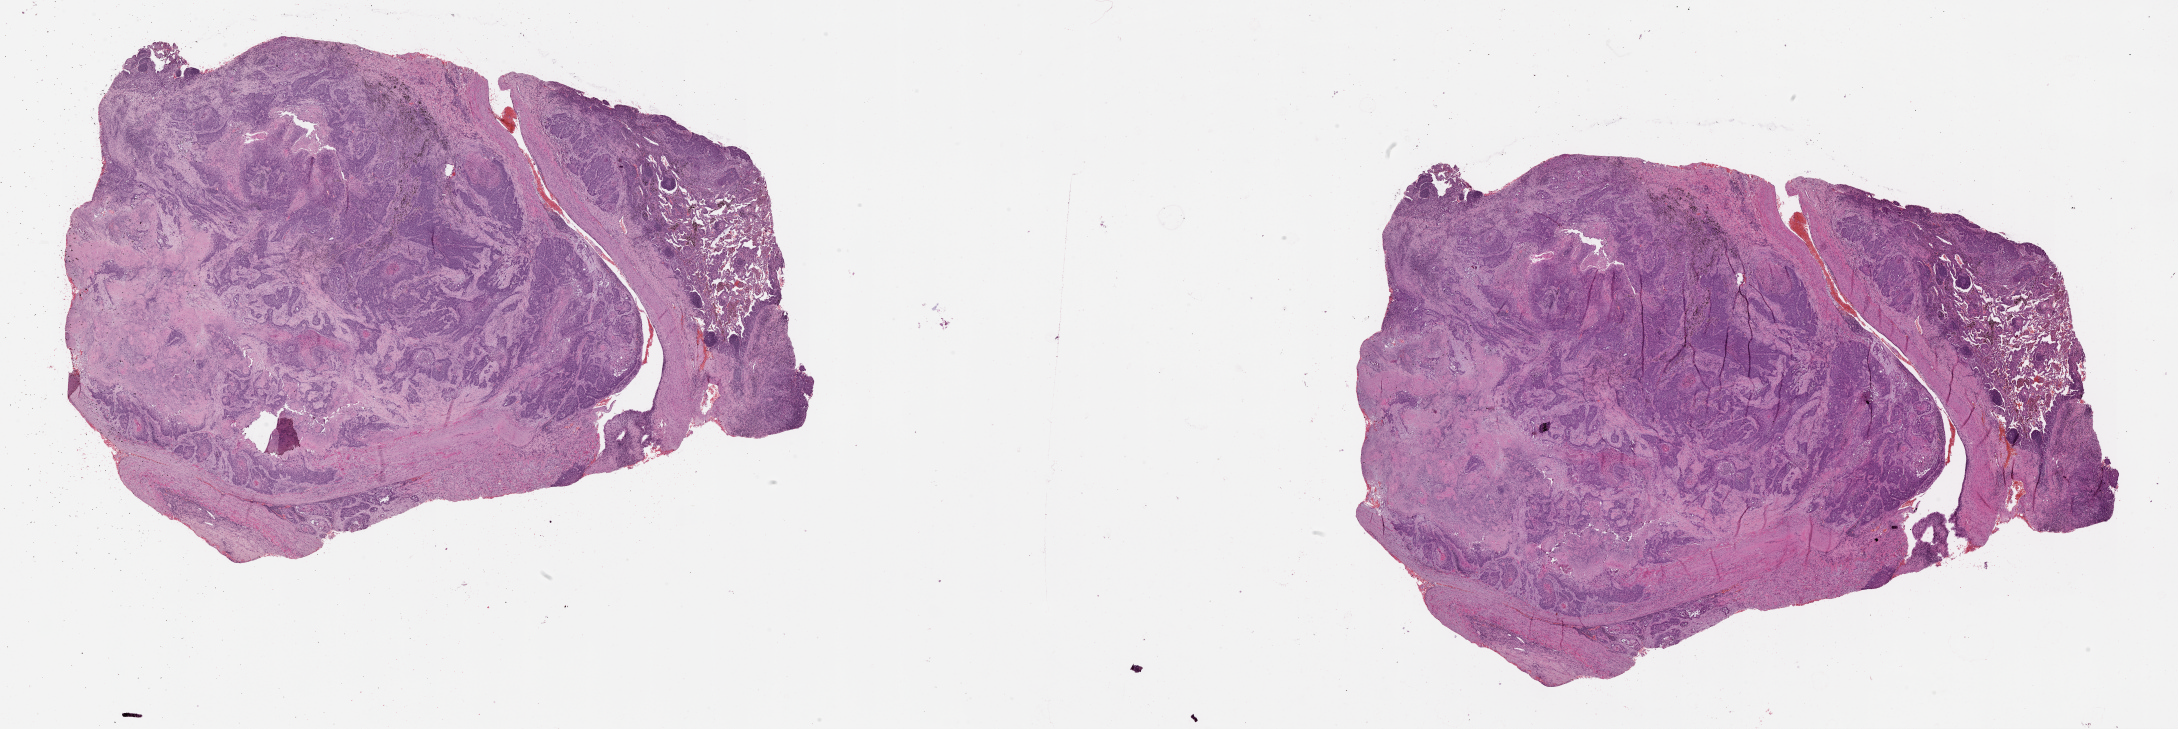
Digitized Hematoxylin and eosin (H&E) stained tissue section (whole slide) — low-resolution overview of the scanned area, about 35.1 x 11.7 mm. Lung, tumour tissue. Male, 59 y/o.
Patient diagnosis (cohort enrolment): squamous cell carcinoma (lung).